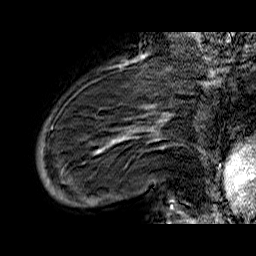
Breast MRI (dynamic contrast-enhanced), one sagittal slice. Dynamic contrast-enhanced series, time point 2 of 6 at this slice position (early post-contrast). 1.5 T. TE 6.5 ms, TR 32.9 ms. 4 mm slice thickness. 256 × 256 image matrix, field of view 200 × 200 mm. Female patient. Case-level facts recorded for this patient, not image findings: setting: breast cancer imaged before/during neoadjuvant chemotherapy; receptor status: HR-positive, HER2-negative.
Annotated regions visible in this slice (semi-automatic segmentation, software-assisted and operator-edited):
- analysis volume of interest (the breast-tissue region the enhancement analysis was run in; not a lesion): bounding box <37,74,176,210> (left, top, right, bottom; pixels)
- tumour enhancement mask (voxels above the 100 % enhancement threshold inside the analysis volume of interest): <41,108,172,209>